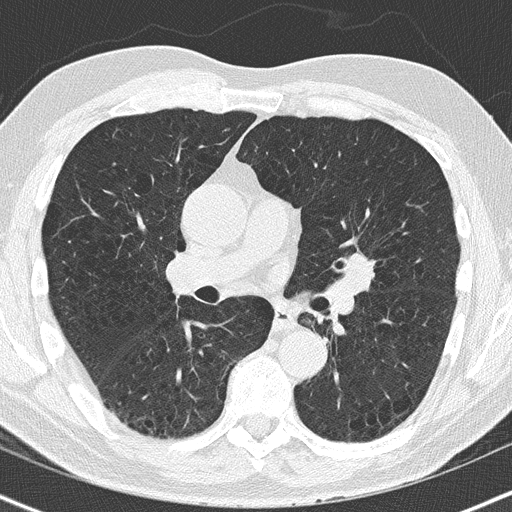
Low-dose screening chest CT, axial slice. Baseline screening round. Lung window (W 1500 / L -600 HU). 2 mm slice thickness. Lung (sharp) reconstruction kernel (B50f). Male participant, aged 63 years at enrolment. Former smoker at enrolment.
Expert reader's lesion annotation, bounding box [x1, y1, x2, y2] px = [334, 254, 380, 292]. The screening reader recorded 2 non-calcified nodules or masses ≥4 mm on this exam; which of them this box marks is not recorded. Participant outcome: lung cancer diagnosed 32 days after this screen — squamous cell carcinoma, NOS, left upper lobe, moderately differentiated (G2), stage IA (AJCC 6th edition), 23 mm at pathology.